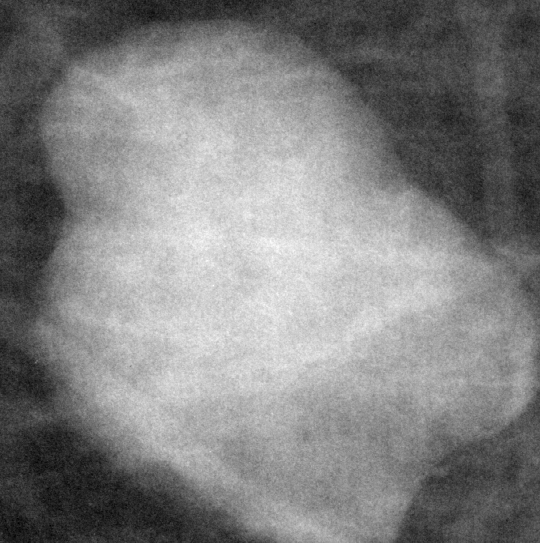
Cropped region of a digitized screen-film mammogram centred on a radiologist-marked abnormality; right breast; CC view; BI-RADS breast density category 1 (scale 1–4).
Finding: mass, shape lobulated, margins circumscribed; BI-RADS assessment category 4; subtlety rating 5 on a 1 (subtle) to 5 (obvious) scale; pathology result (as recorded, not read from the image): benign.